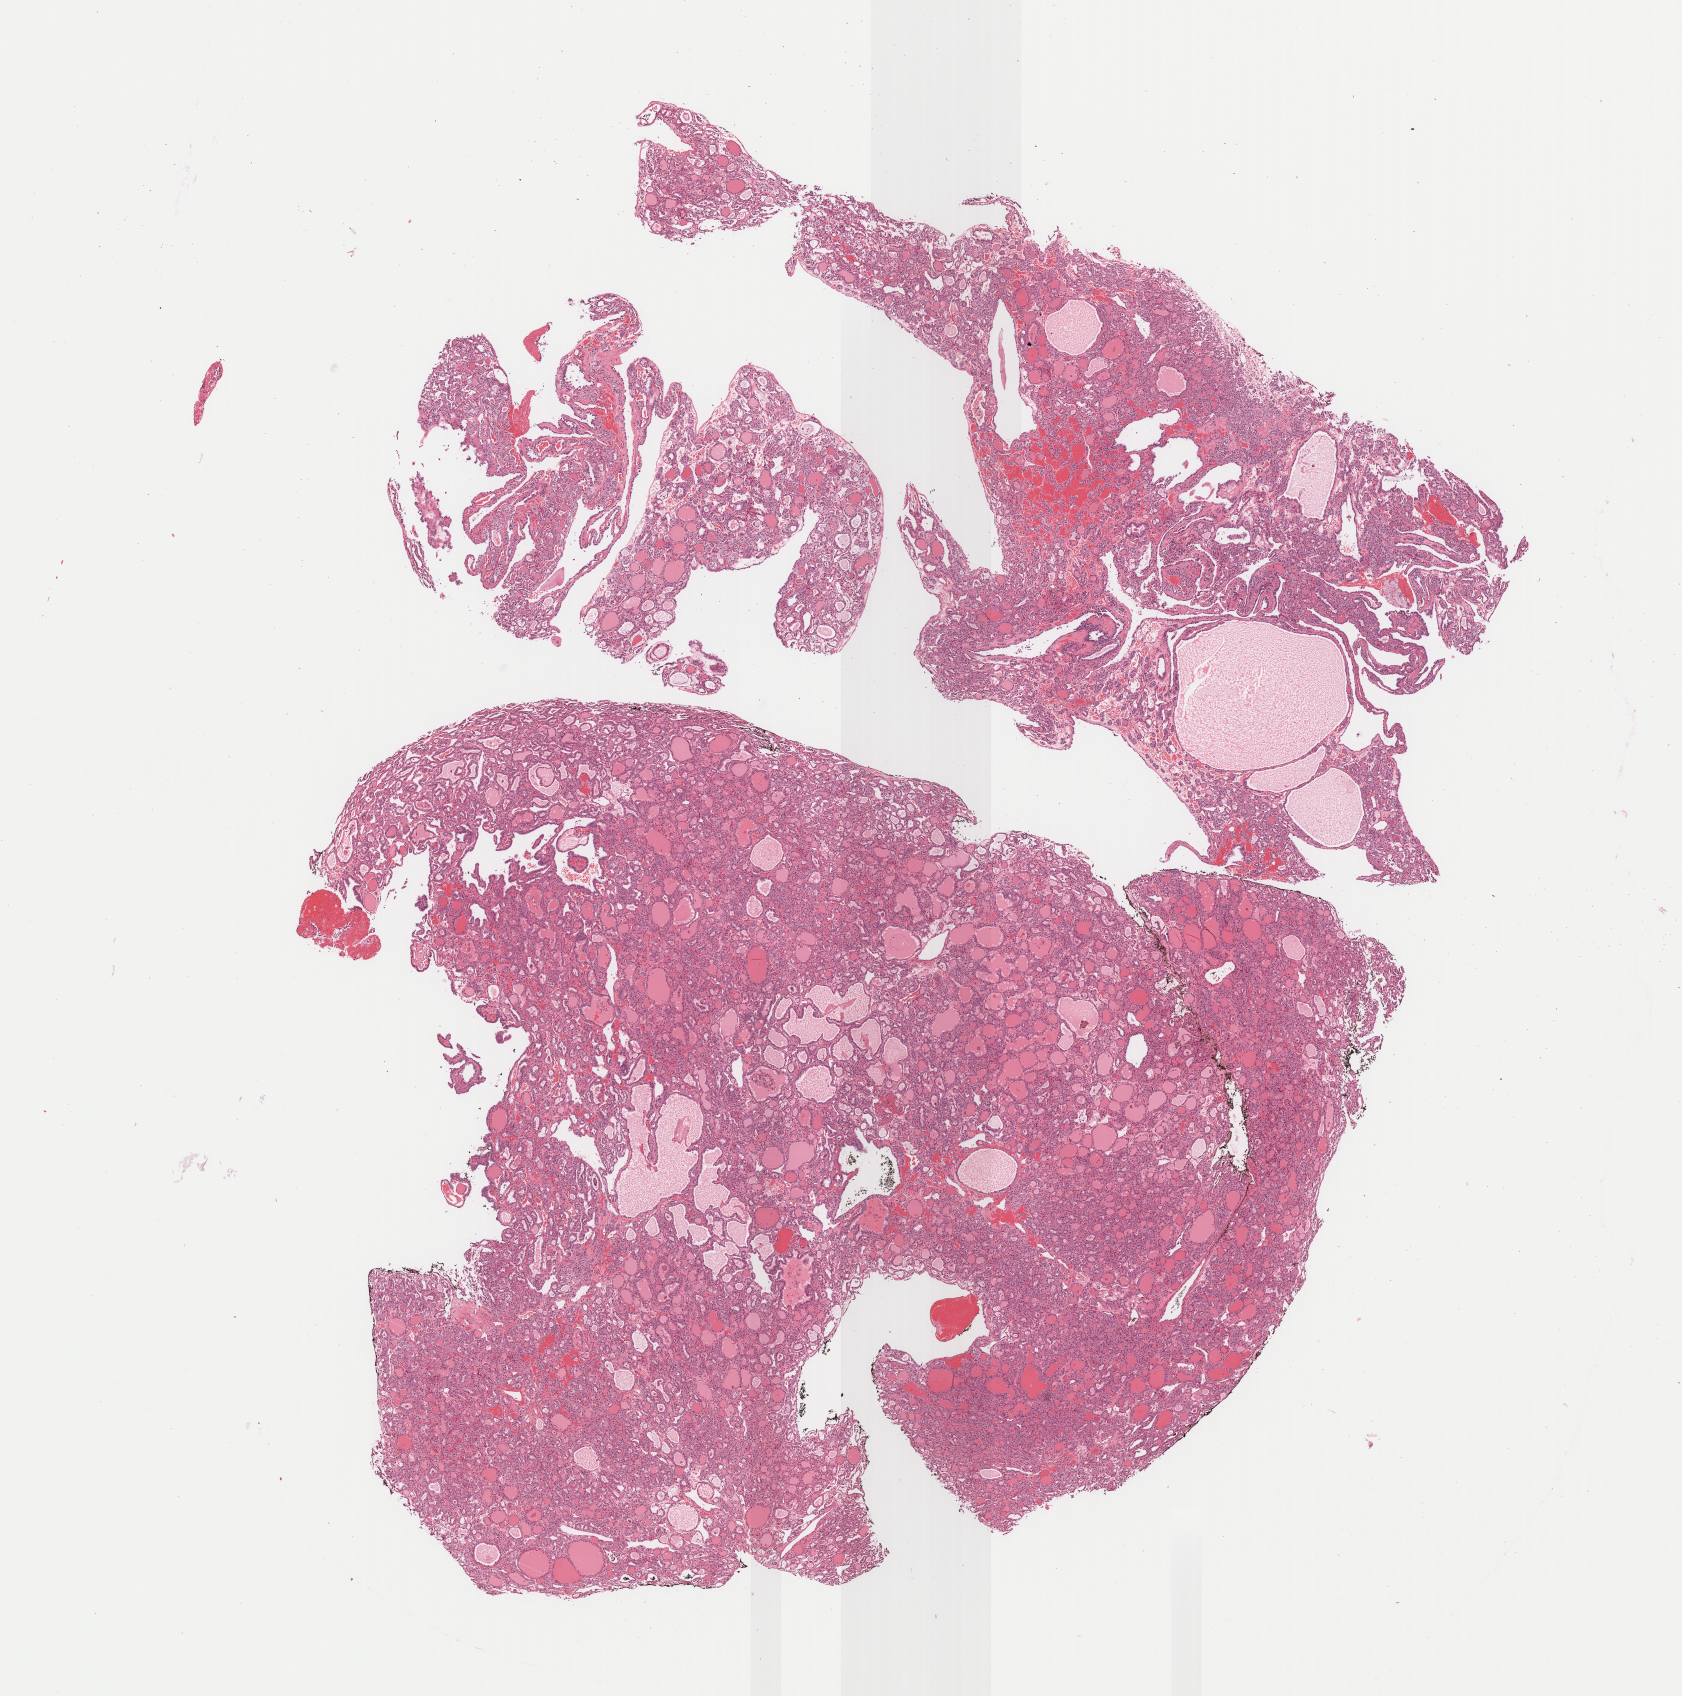
Digitized H&E-stained tissue section (whole slide), whole scanned area (about 13.5 x 13.7 mm) shown as a low-resolution overview, FFPE section, sample: primary tumour, thyroid. Female patient; age at initial diagnosis 46 years.
• laterality: right
• diagnosis: Papillary carcinoma, follicular variant
• AJCC pathologic stage: II (7th edition)
• TNM: T2 N0 MX